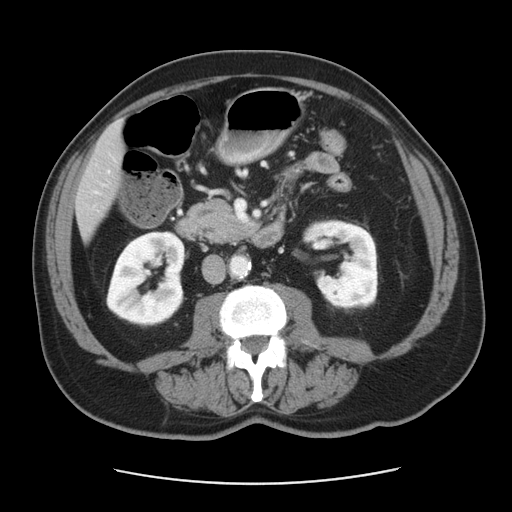
Contrast-enhanced abdominal CT, one axial slice; slice 14 of 42 in the series (ordered by position); intravenous contrast given; soft-tissue window (W 400 / L 40 HU); 5 mm slice thickness; 512 × 512 image matrix, field of view 370 × 370 mm. Male patient, age 73 years. Case-level facts recorded for this patient, not image findings: diagnosis: colorectal cancer liver metastases, imaged before liver resection; multiple liver metastases: yes; largest metastasis: 0.5 cm; disease in both lobes: no.
Annotated regions visible in this slice (outlined manually by an expert reader):
- liver: bounding box [x1, y1, x2, y2] px = [77, 127, 122, 236]
- planned liver remnant (the part of the liver to remain after resection): [108, 127, 120, 144]